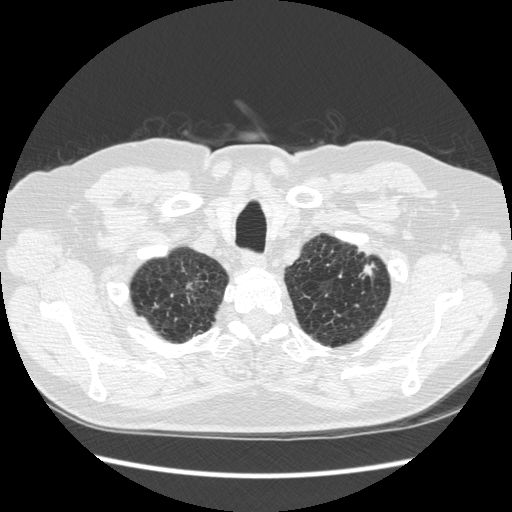
Low-dose screening chest CT, one axial slice; position 243 of 267 along the scan axis; lung window (W 1500 / L -600 HU); 512 × 512 image matrix, field of view 360 × 360 mm.
Structures marked on this image (manually delineated by an expert):
- lesion 1 (tumor, upper lobe of left lung): bounding box (x1, y1, x2, y2) in pixels: (364, 265, 373, 276)